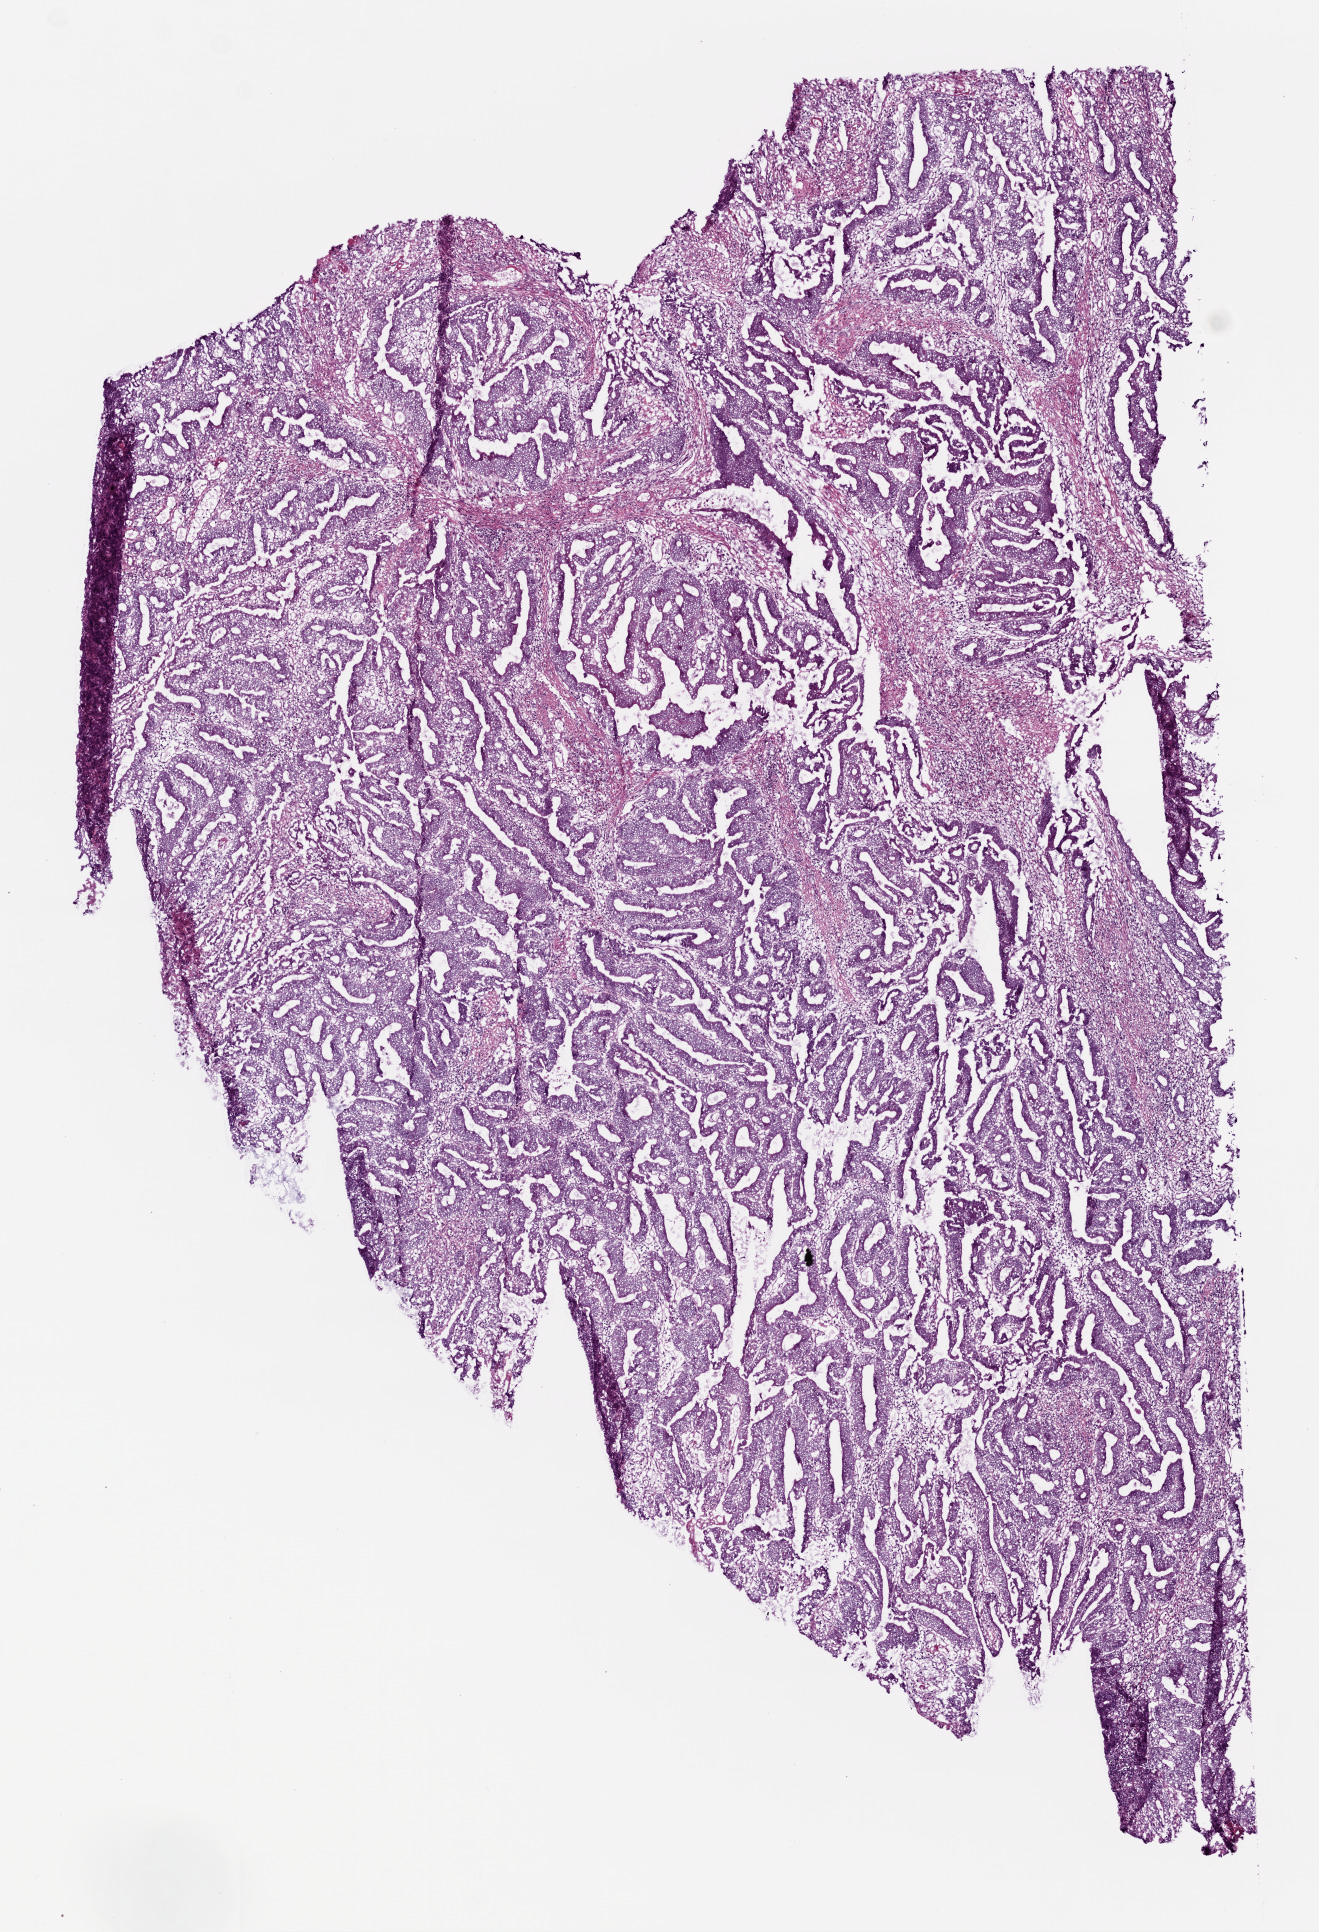
Whole-slide histology image, H&E-stained, whole scanned area (about 5.3 x 7.8 mm, acquisition: 20x scan) shown as a low-resolution overview, frozen section from the bottom of the tissue portion, primary tumour sample from the rectum. Patient: female, age at initial diagnosis 73 years.
Diagnosis: Adenocarcinoma, NOS (rectosigmoid junction).